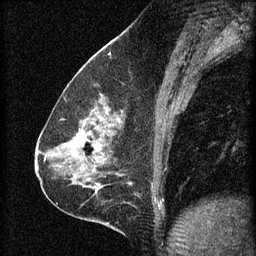
Breast MRI (dynamic contrast-enhanced), one sagittal slice. Slice 31 of 60 in the series (ordered by position). 3 images stored at this slice position (order not interpretable as contrast timing). 1.5 T. TE 4.2 ms, TR 8.2 ms. 2 mm slice thickness. 256 × 256 image matrix. Female patient, age 59 years.
Structures marked on this image (semi-automatic segmentation, software-assisted and operator-edited):
- analysis volume of interest (the breast-tissue region the enhancement analysis was run in; not a lesion): bounding box <61,104,126,161> (left, top, right, bottom; pixels)
- tumour enhancement mask (voxels above the 70 % enhancement threshold inside the analysis volume of interest): <72,110,108,151>